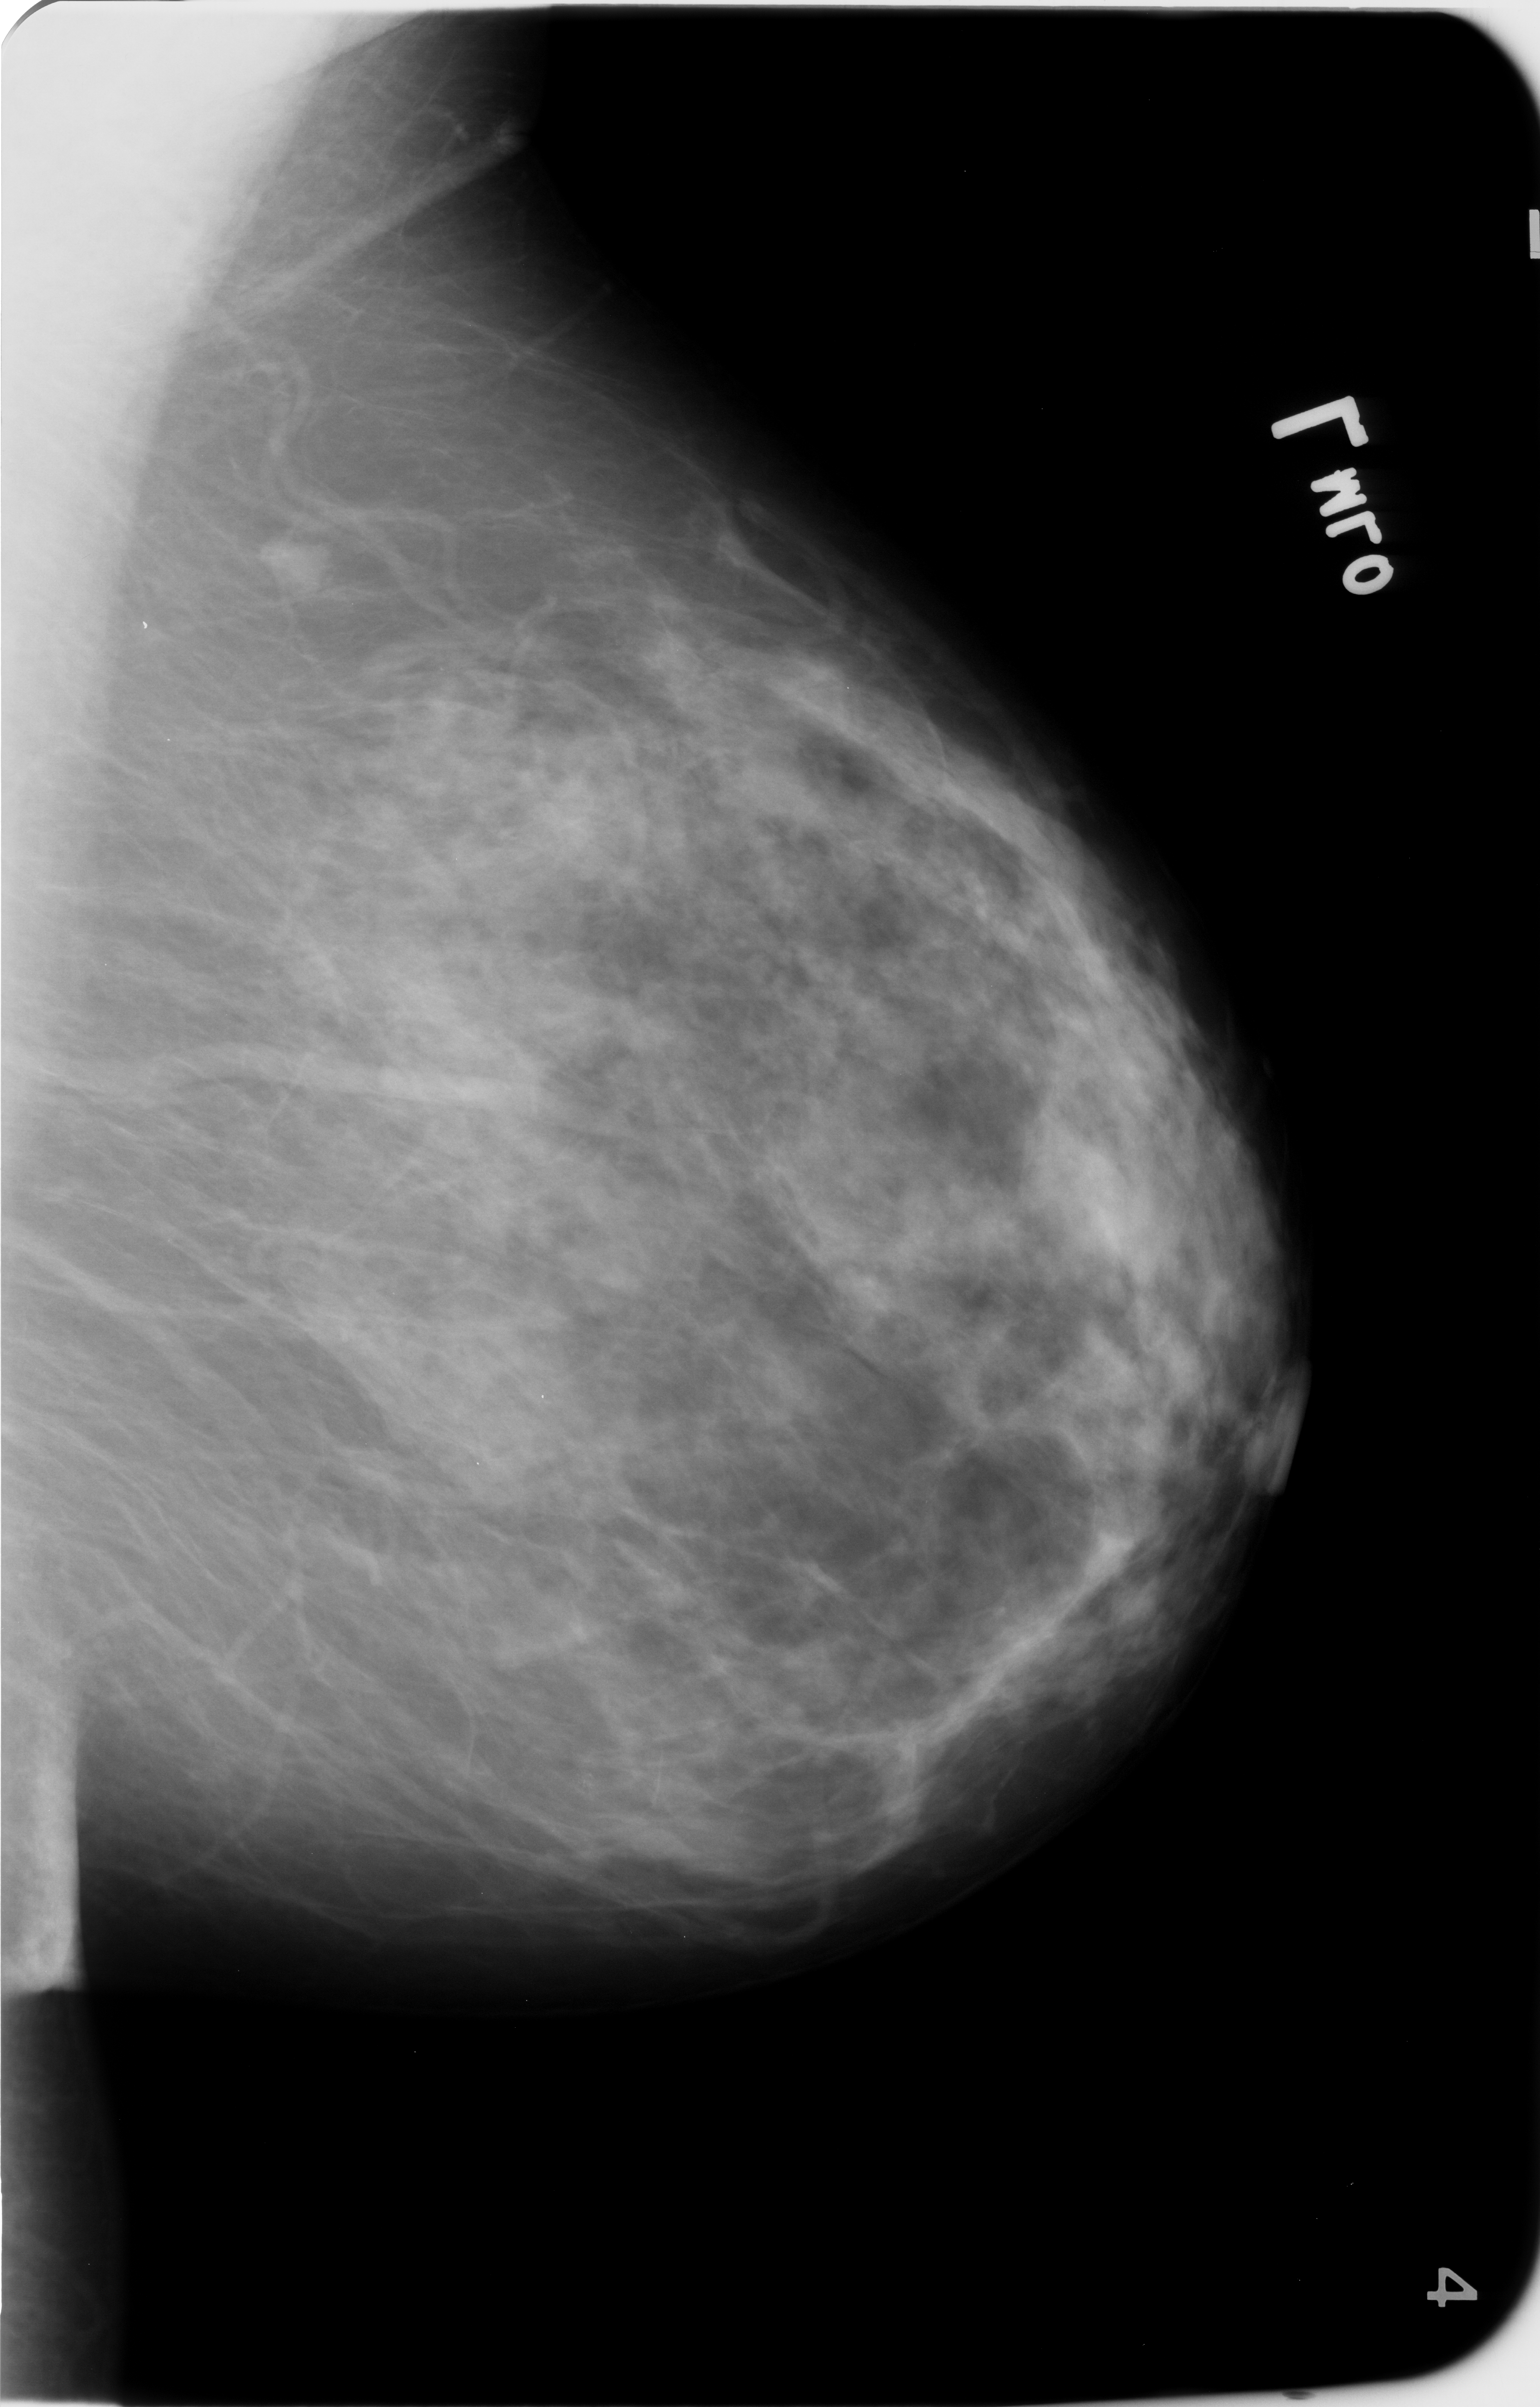
Digitized screen-film mammogram. Left breast. Mediolateral oblique (MLO) view. BI-RADS breast density category 2 (scale 1–4). 1540 × 2407 image matrix.
Expert-marked regions of interest on this film, with their recorded descriptors:
- calcifications, morphology pleomorphic, distribution clustered; BI-RADS assessment category 4; pathology result (as recorded, not read from the image): benign: bounding box <550,1746,632,1837> (left, top, right, bottom; pixels)